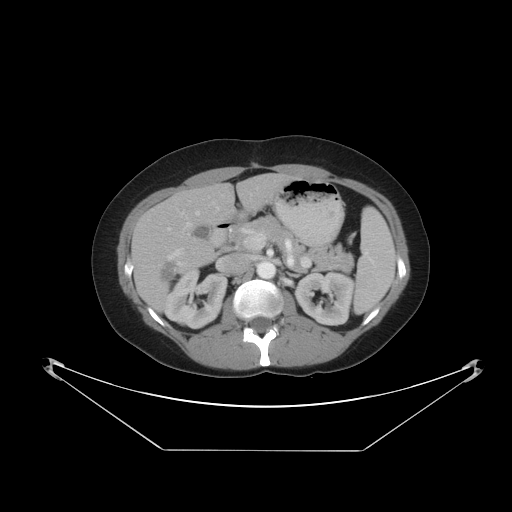
Contrast-enhanced abdominal CT, one axial slice. Position 24 of 48 along the scan axis. 120 kVp. Intravenous contrast given. Soft-tissue window (W 400 / L 40 HU). 512 × 512 image matrix, field of view 482 × 482 mm. Female patient, age 38 years. Case-level facts recorded for this patient, not image findings: diagnosis: colorectal cancer liver metastases, imaged before liver resection; multiple liver metastases: yes; largest metastasis: 2.5 cm.
Structures marked on this image (outlined manually by an expert reader):
- hepatic veins: box from (x=185, y=211) to (x=200, y=228) px
- liver: (x=132, y=175)–(x=294, y=312)
- planned liver remnant (the part of the liver to remain after resection): (x=168, y=175)–(x=295, y=226)
- portal vein (with intrahepatic branches): (x=168, y=207)–(x=219, y=266)
- liver metastasis: (x=161, y=261)–(x=182, y=284)